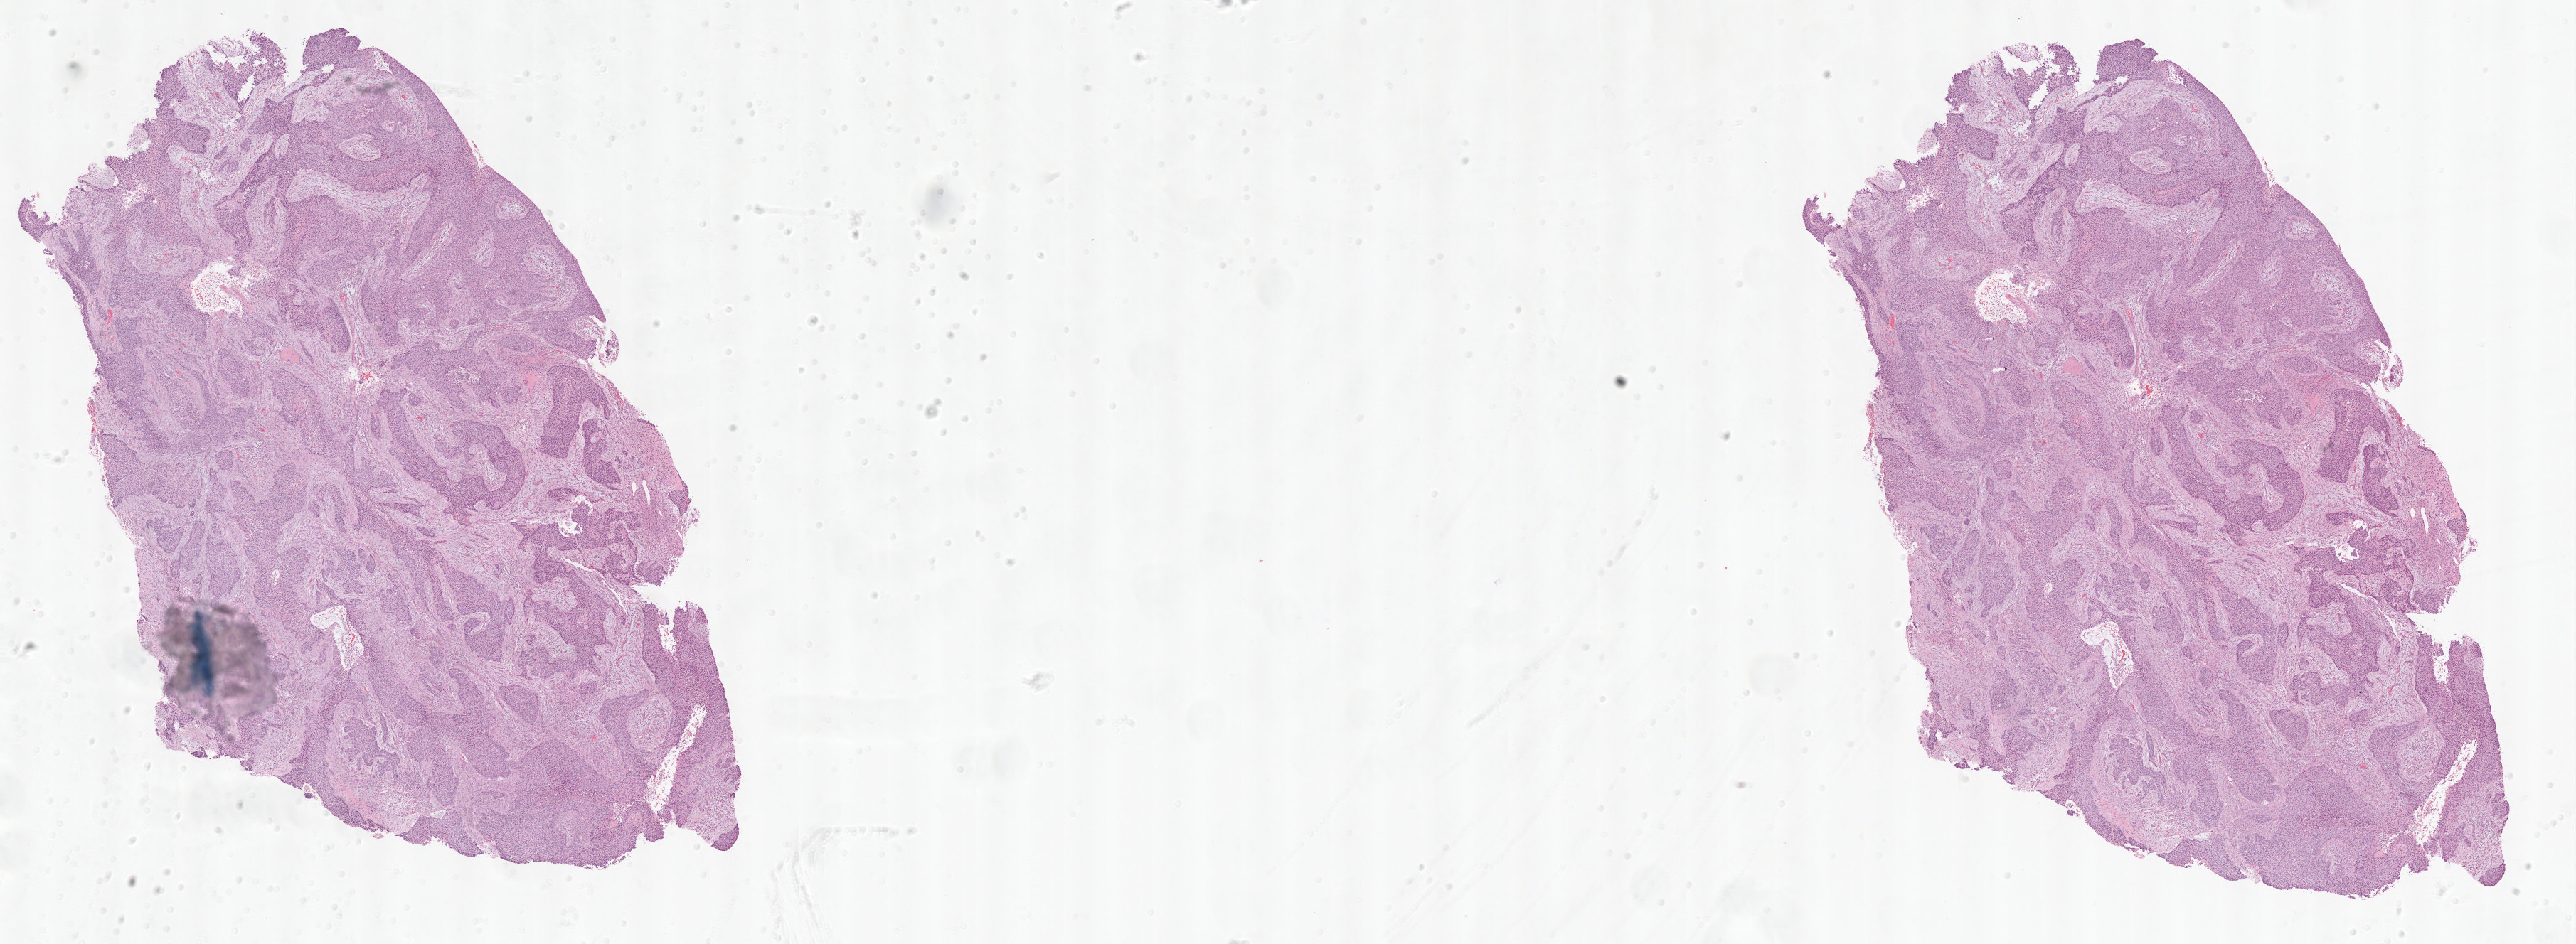
Digitized Hematoxylin and eosin (H&E) stained tissue section (whole slide) — shown as a low-resolution overview of the whole scanned area (about 29.0 x 10.6 mm); formalin-fixed paraffin-embedded (FFPE) diagnostic section; primary tumour sample from the lung. Male patient; age at initial diagnosis 76 years.
- AJCC pathologic stage: IB (6th edition)
- TNM: T2 N0 M0
- laterality: right
- pathologic diagnosis: Squamous cell carcinoma, NOS (upper lobe, lung)